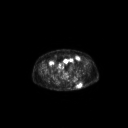
FDG PET of an extremity soft-tissue mass (from a PET/CT study), one axial slice; 3.27 mm slice thickness; 128 × 128 image matrix. Patient: male, 69 years. Case-level facts recorded for this patient, not image findings: histological type: leiomyosarcoma; grade: intermediate; site of the primary tumour: left pelvis.
Annotated regions visible in this slice (expert contour drawn on MRI and transferred to this co-registered scan by the dataset authors):
- gross tumour volume (mass): bounding box <76,82,83,88> (left, top, right, bottom; pixels)